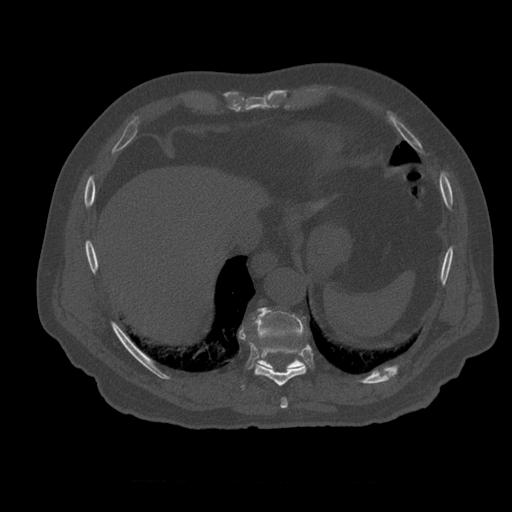
CT including the spine, one axial slice. Slice 315 of 399 in the series (ordered by position). Reconstruction kernel STANDARD. Bone window (W 1800 / L 400 HU). 1.25 mm slice thickness. 512 × 512 image matrix, field of view 407 × 407 mm. Patient age 73 years. Case-level facts recorded for this patient, not image findings: primary cancer: prostate; vertebrae with lytic lesions (as recorded): L2.
Outlined on this slice (semi-automatically segmented with operator editing):
- T10 vertebra: box from (x=253, y=307) to (x=307, y=370) px
- T12 vertebra: (x=270, y=350)–(x=277, y=355)
- T8 vertebra: (x=281, y=398)–(x=288, y=409)
- T9 vertebra: (x=255, y=340)–(x=307, y=387)